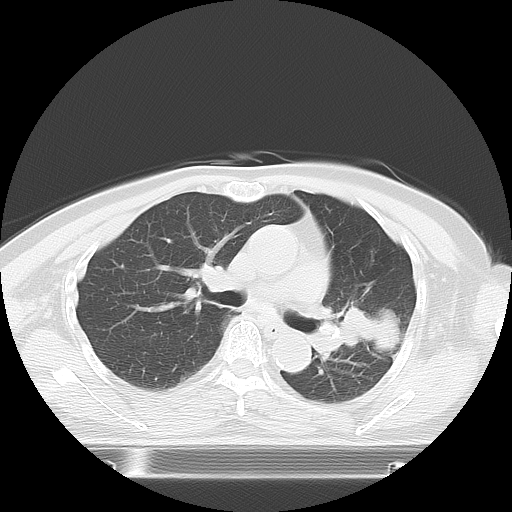
Chest CT, one axial slice. Position 1 of 21 along the scan axis. Reconstruction kernel LUNG. 120 kVp. Lung window (W 1500 / L -600 HU). 512 × 512 image matrix, field of view 350 × 350 mm. Patient: female, 74 years. From the clinical record (not read from this slice): clinical TNM (as recorded): T3 N1 M1c; histopathological grade: G3.
Outlined on this slice (rectangle marked by the reading radiologist):
- lung tumour (recorded histology: small cell carcinoma): box from (x=333, y=304) to (x=404, y=365) px